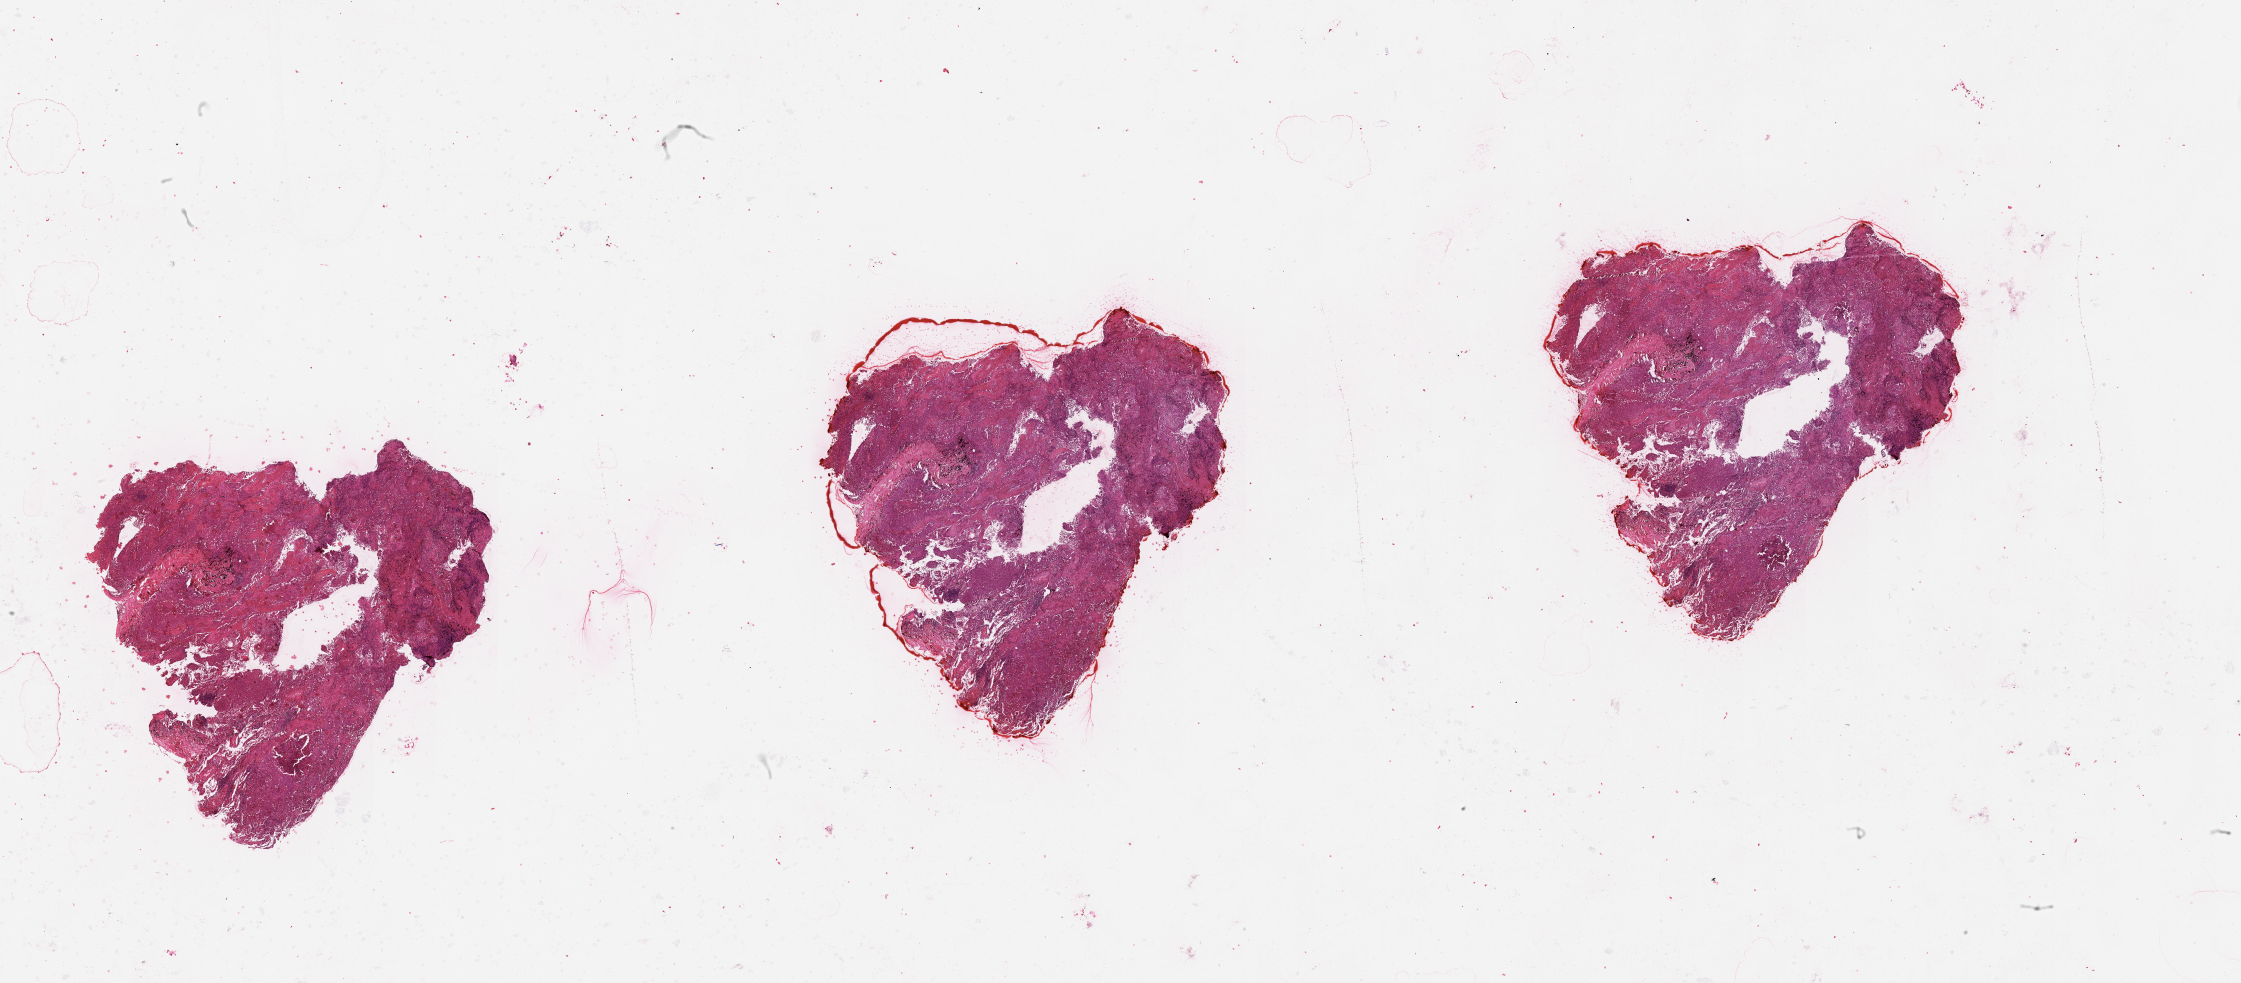
Whole-slide histology image, H&E-stained, shown as a low-resolution overview of the whole scanned area (about 36.1 x 15.8 mm, from a 20x scan); lung, tissue type not recorded.
Patient diagnosis (cohort enrolment): squamous cell carcinoma (lung).